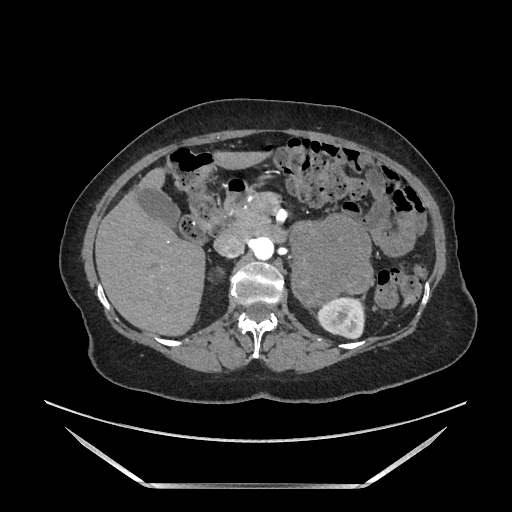
Contrast-enhanced abdominal CT, one axial slice; position 100 of 205 along the scan axis; soft-tissue window (W 400 / L 40 HU); 1.25 mm slice thickness; 512 × 512 image matrix, field of view 440 × 440 mm. Female patient. From the clinical record (not read from this slice): diagnosis: adrenocortical carcinoma; tumour side: left adrenal; tumour size at pathology: 12.5 cm; Ki-67 index: 39 %; stage (as recorded): 3.
Outlined on this slice (semi-automatic segmentation, software-assisted and operator-edited):
- mass: bounding box <291,216,373,303> (left, top, right, bottom; pixels)